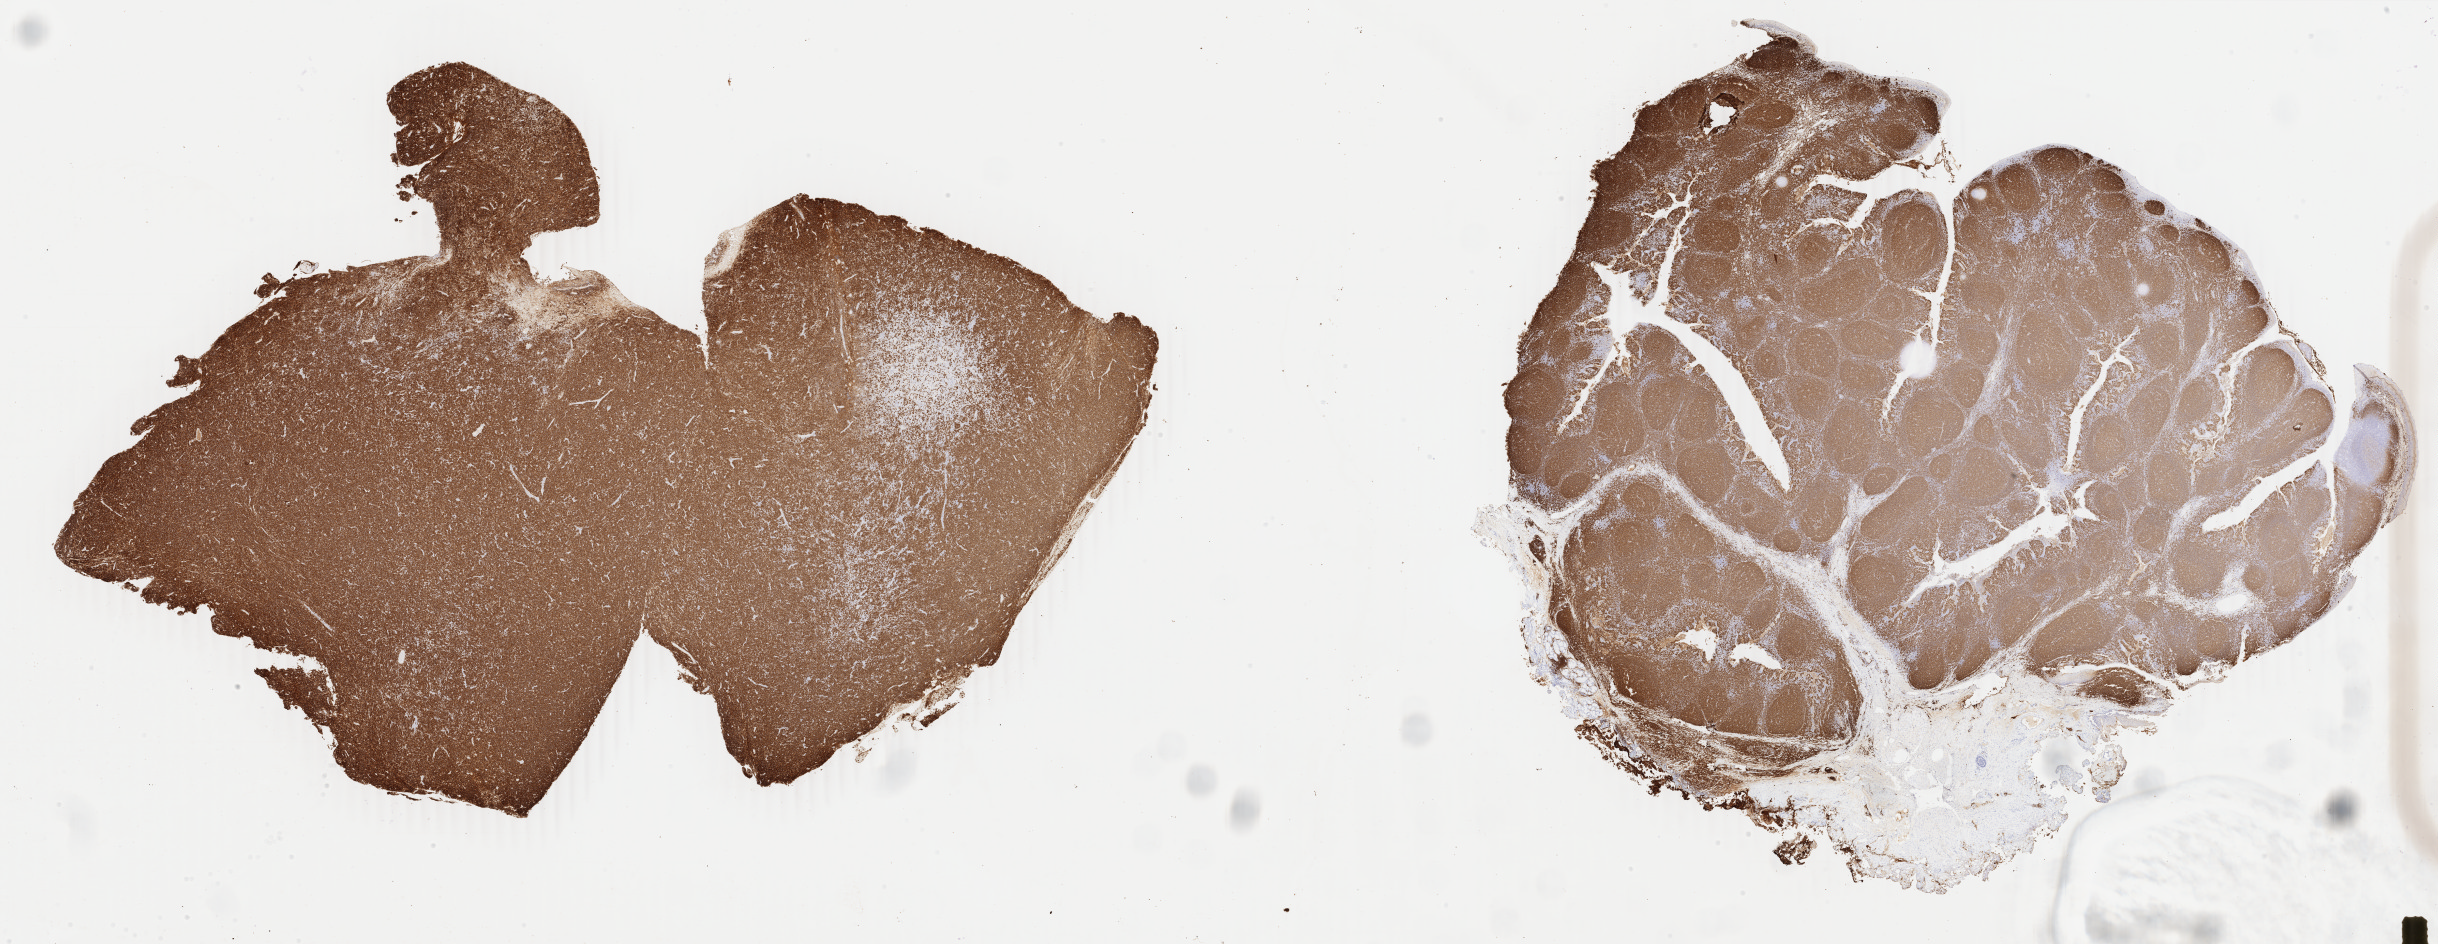
IHC for CD20, whole-slide image, whole scanned area (about 38.8 x 15.0 mm) shown as a low-resolution overview. Tumor tissue. Patient: male, age at initial diagnosis 7 years.
Histologic diagnosis: Diffuse large B-cell lymphoma, NOS.